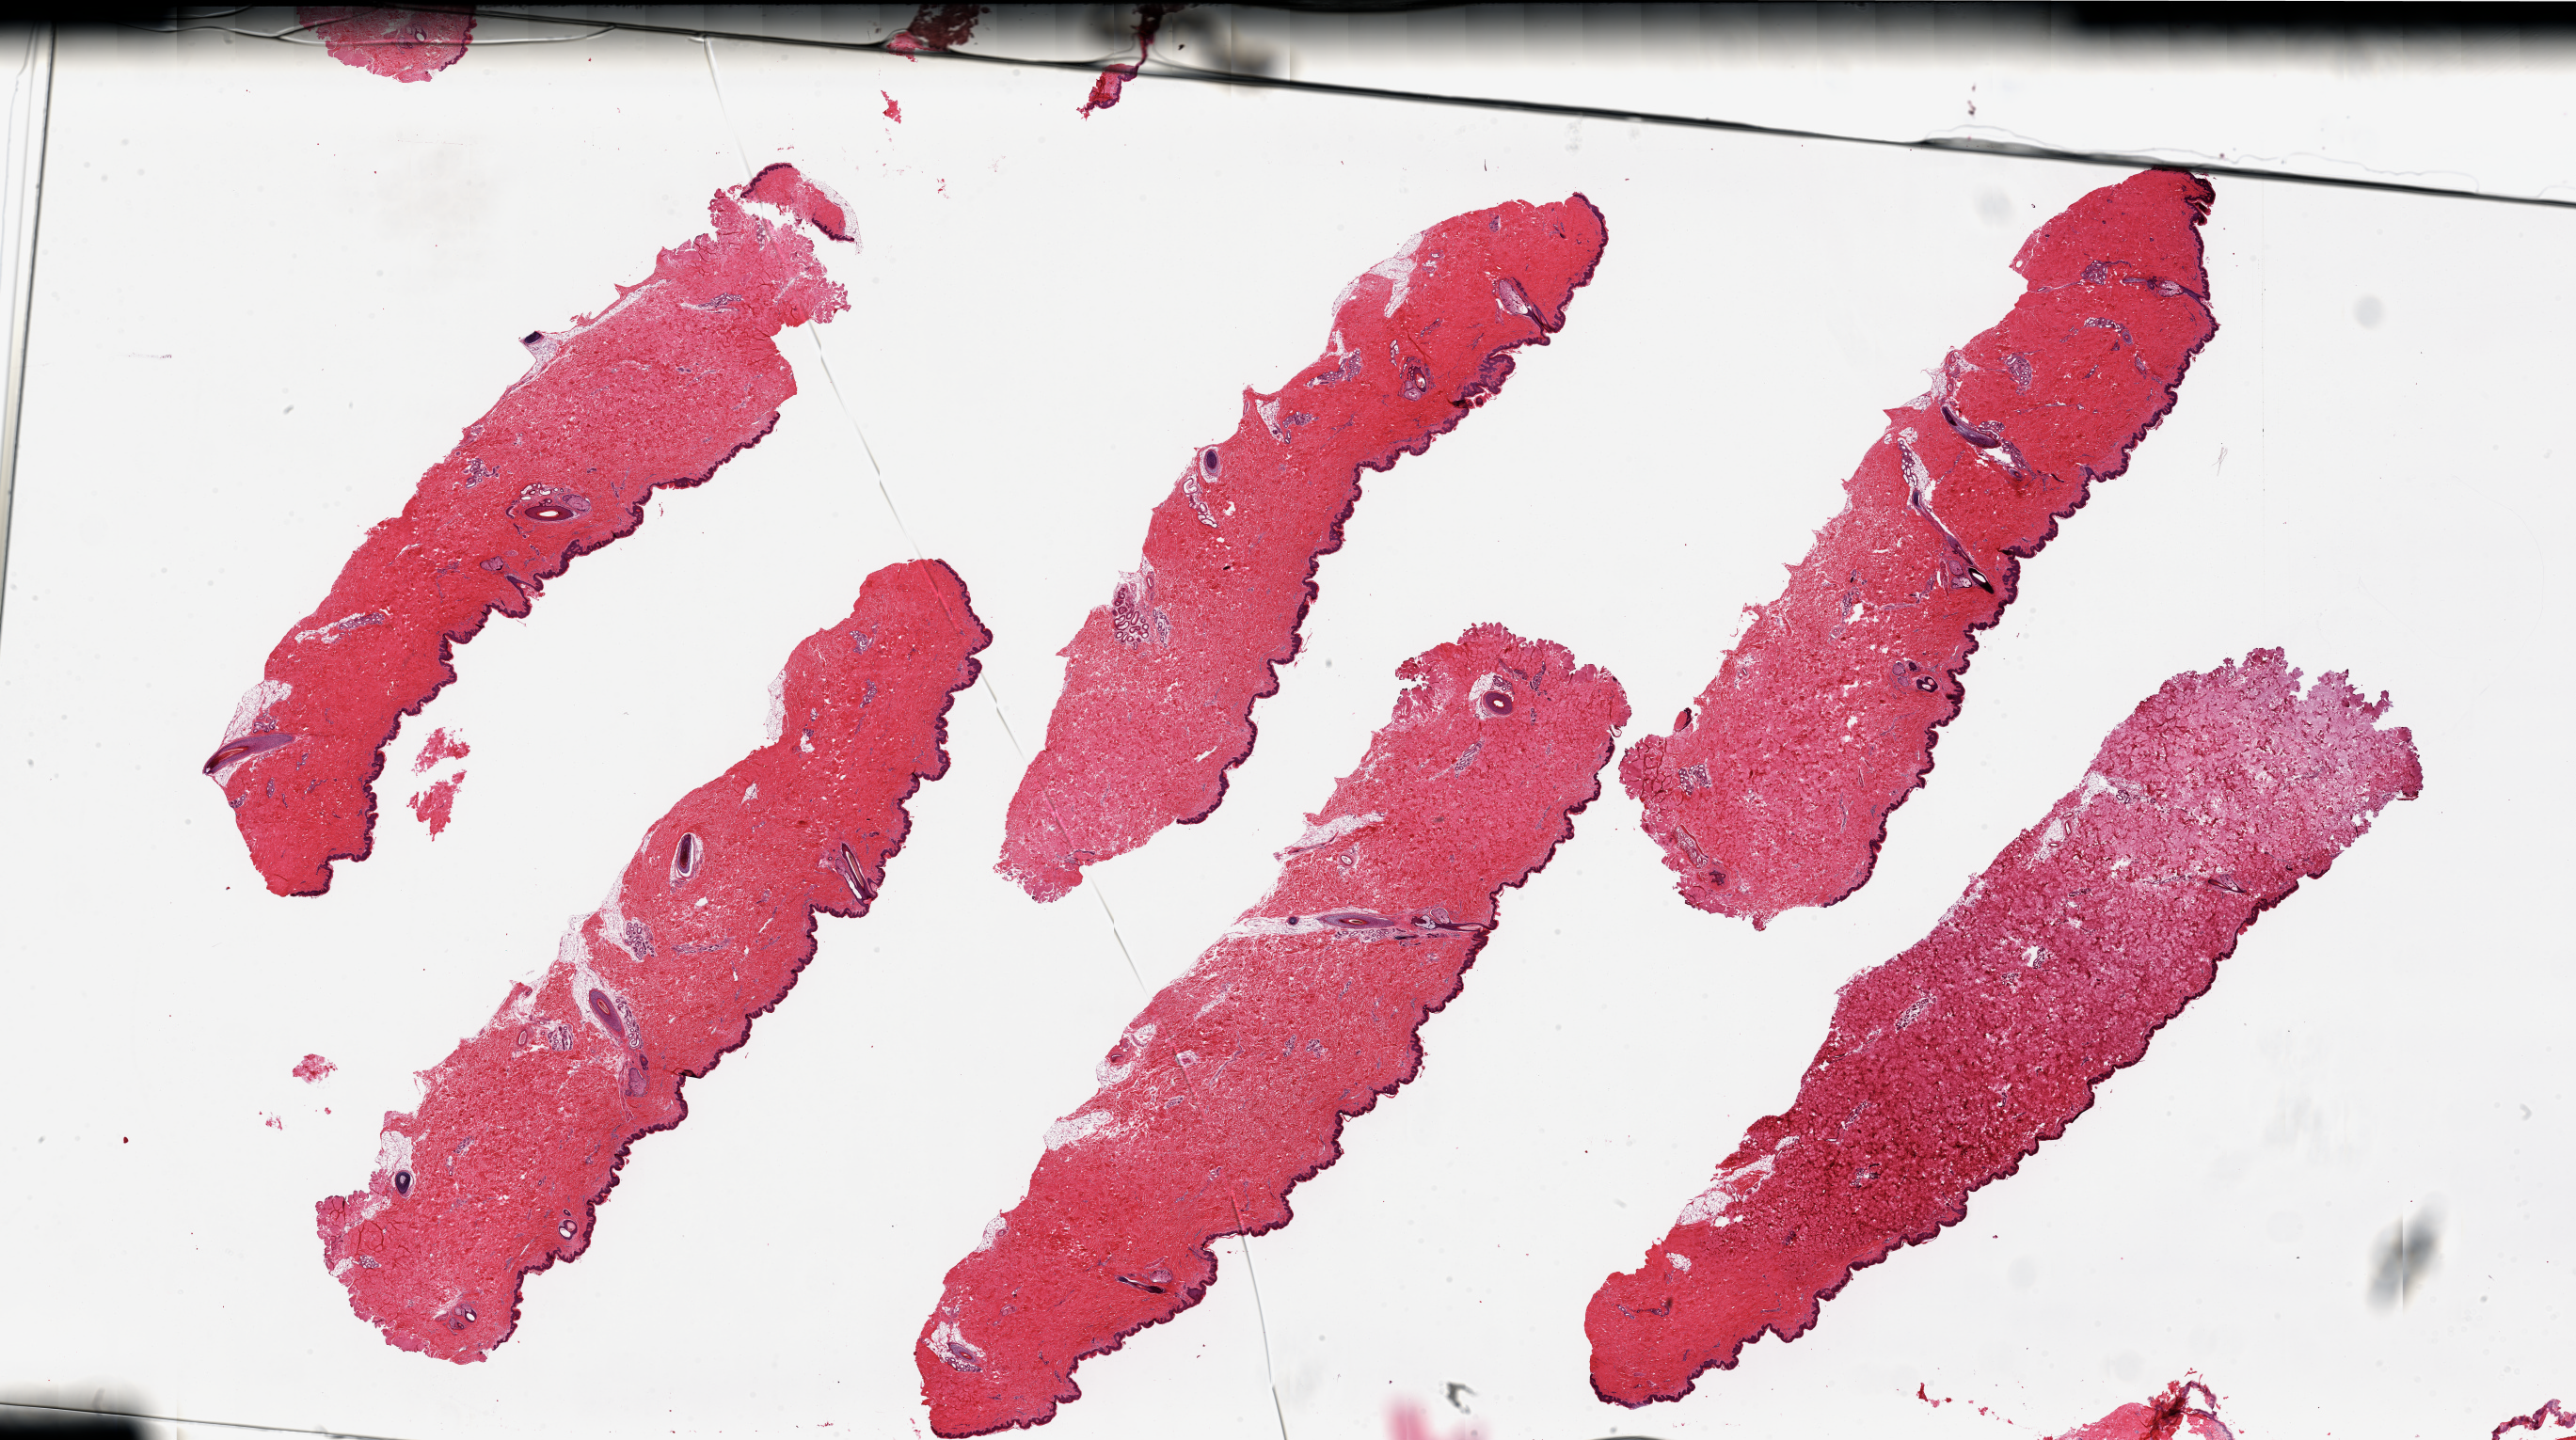
Whole-slide image, H&E stain, whole scanned area (about 43.3 x 24.2 mm) shown as a low-resolution overview; PAXgene-fixed, paraffin-embedded tissue; section of skin of suprapubic region (target tissue); donor tissue sample. Male donor.
* pathologist's review note for this sample: 6 pieces, minimal subcutaneous fat; squamous epithelium is ~0.1mm thick